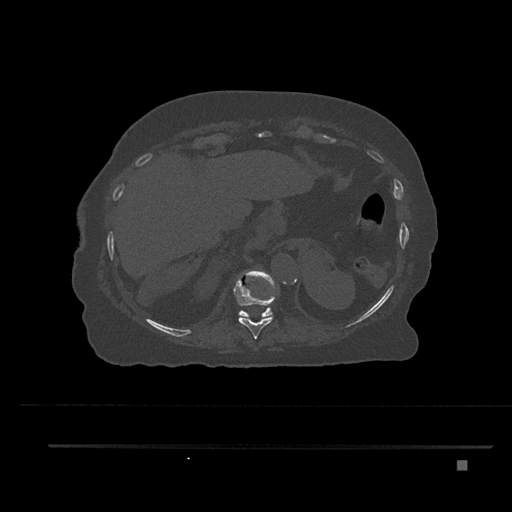
CT including the spine, one axial slice. Slice 341 of 797 in the series (ordered by position). Bone window (W 1800 / L 400 HU). 0.5 mm slice thickness. 512 × 512 image matrix, field of view 437 × 437 mm. Patient: female, 76 years. From the clinical record (not read from this slice): primary cancer: lung; vertebrae with lytic lesions (as recorded): T11, L3.
Structures marked on this image (semi-automatic segmentation, software-assisted and operator-edited):
- T10 vertebra: bounding box [x1, y1, x2, y2] px = [233, 278, 276, 339]
- T11 vertebra: [238, 270, 277, 318]